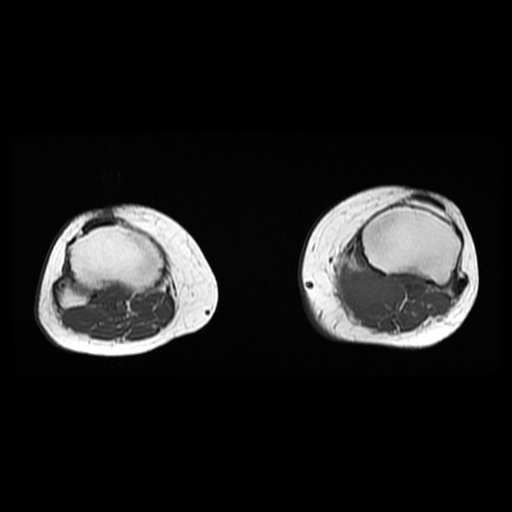
MRI of an extremity soft-tissue mass, one axial slice; position 24 of 38 along the scan axis; 512 × 512 image matrix, field of view 330 × 330 mm. Female patient. From the clinical record (not read from this slice): histological type: extraskeletal high grade osteogenic sarcoma; grade: high; site of the primary tumour: left calf.
Outlined on this slice (outlined manually by an expert reader):
- gross tumour volume (mass): bounding box (x1, y1, x2, y2) in pixels: (334, 264, 397, 313)